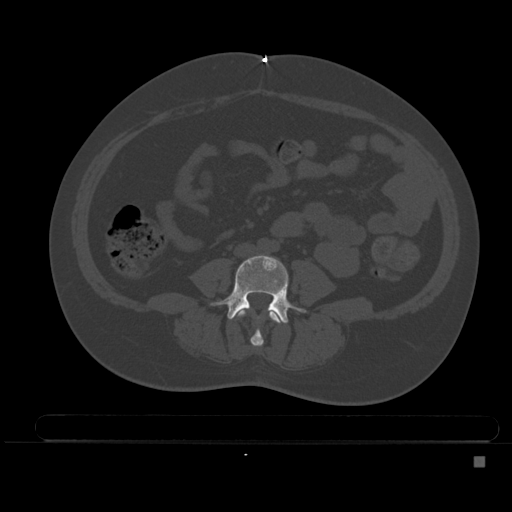
CT including the spine, one axial slice; slice 135 of 495 in the series (ordered by position); bone window (W 1800 / L 400 HU); 512 × 512 image matrix, field of view 404 × 404 mm. Female patient, age 33 years. Case-level facts recorded for this patient, not image findings: primary cancer: breast; vertebrae with lytic lesions (as recorded): T1.
Structures marked on this image (semi-automatic segmentation, software-assisted and operator-edited):
- L3 vertebra: bounding box (x1, y1, x2, y2) in pixels: (236, 309, 283, 347)
- L4 vertebra: (214, 254, 305, 324)